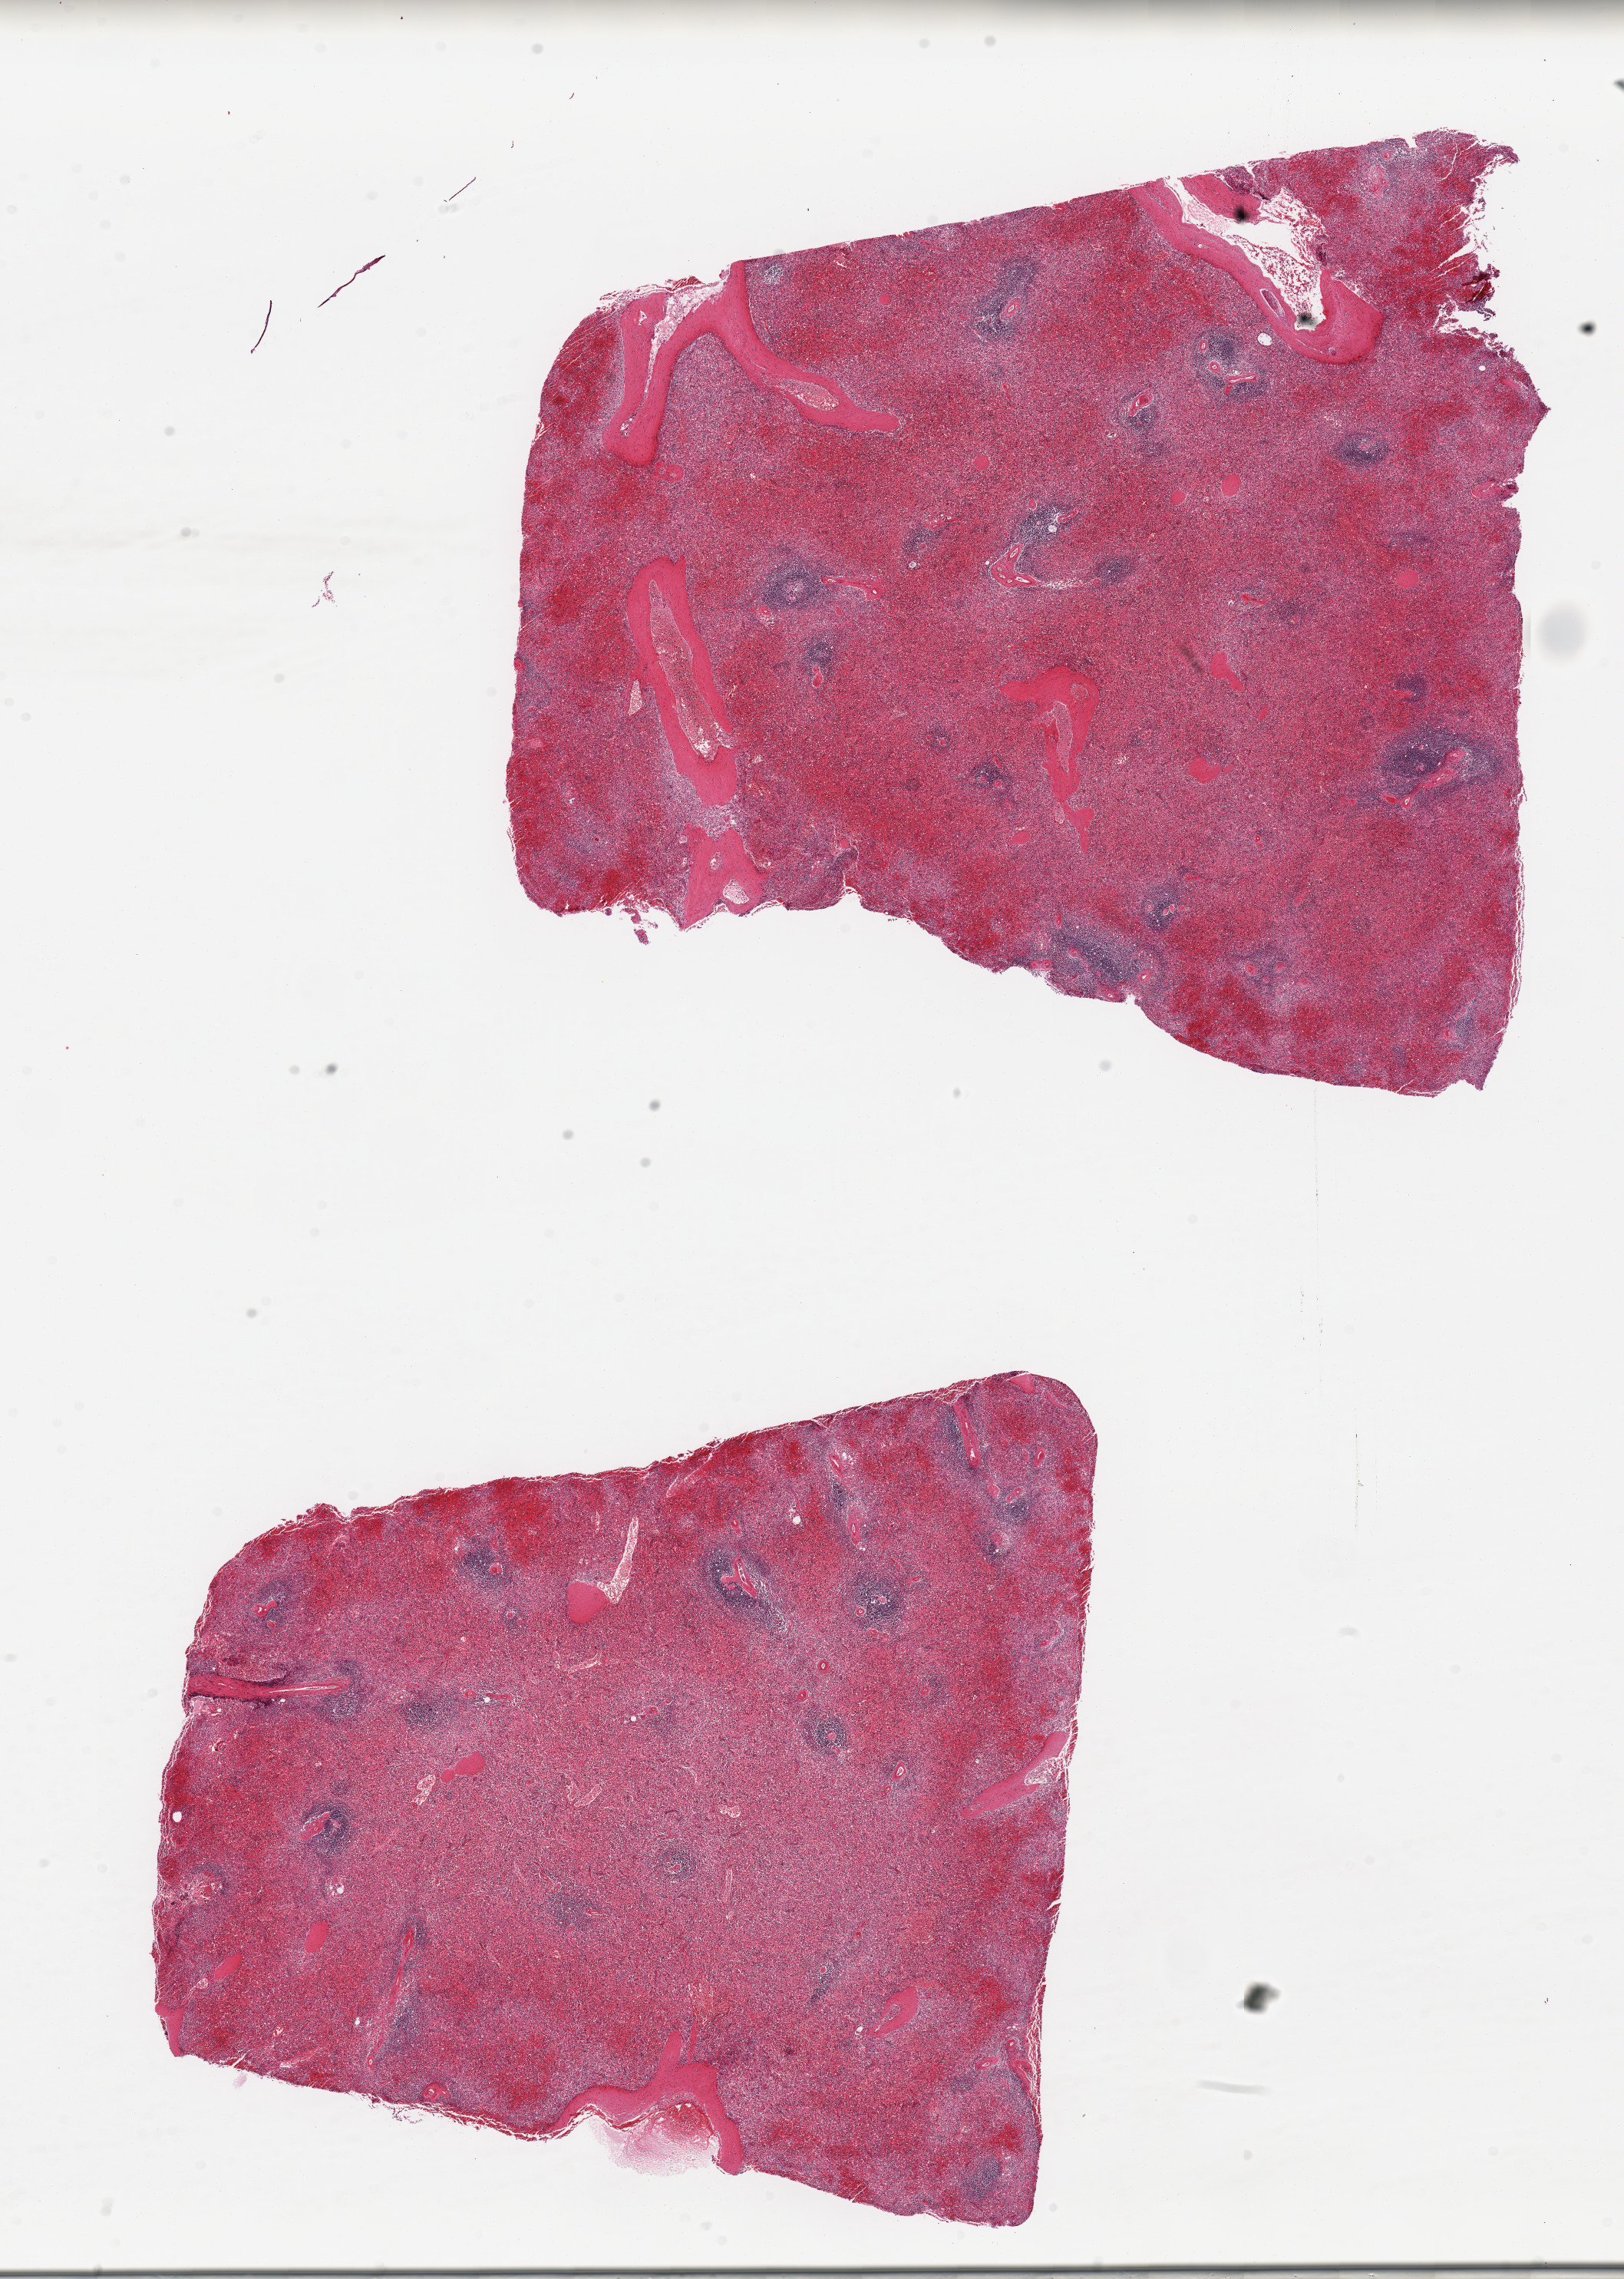
Hematoxylin and eosin (H&E) whole-slide image — whole scanned area (about 16.7 x 23.5 mm) shown as a low-resolution overview; PAXgene-fixed paraffin-embedded (PFPE) section; sampled site (target tissue): spleen; tissue donor sample. Donor sex: male.
Review note (as recorded): 2 pieces; moderate congestion.